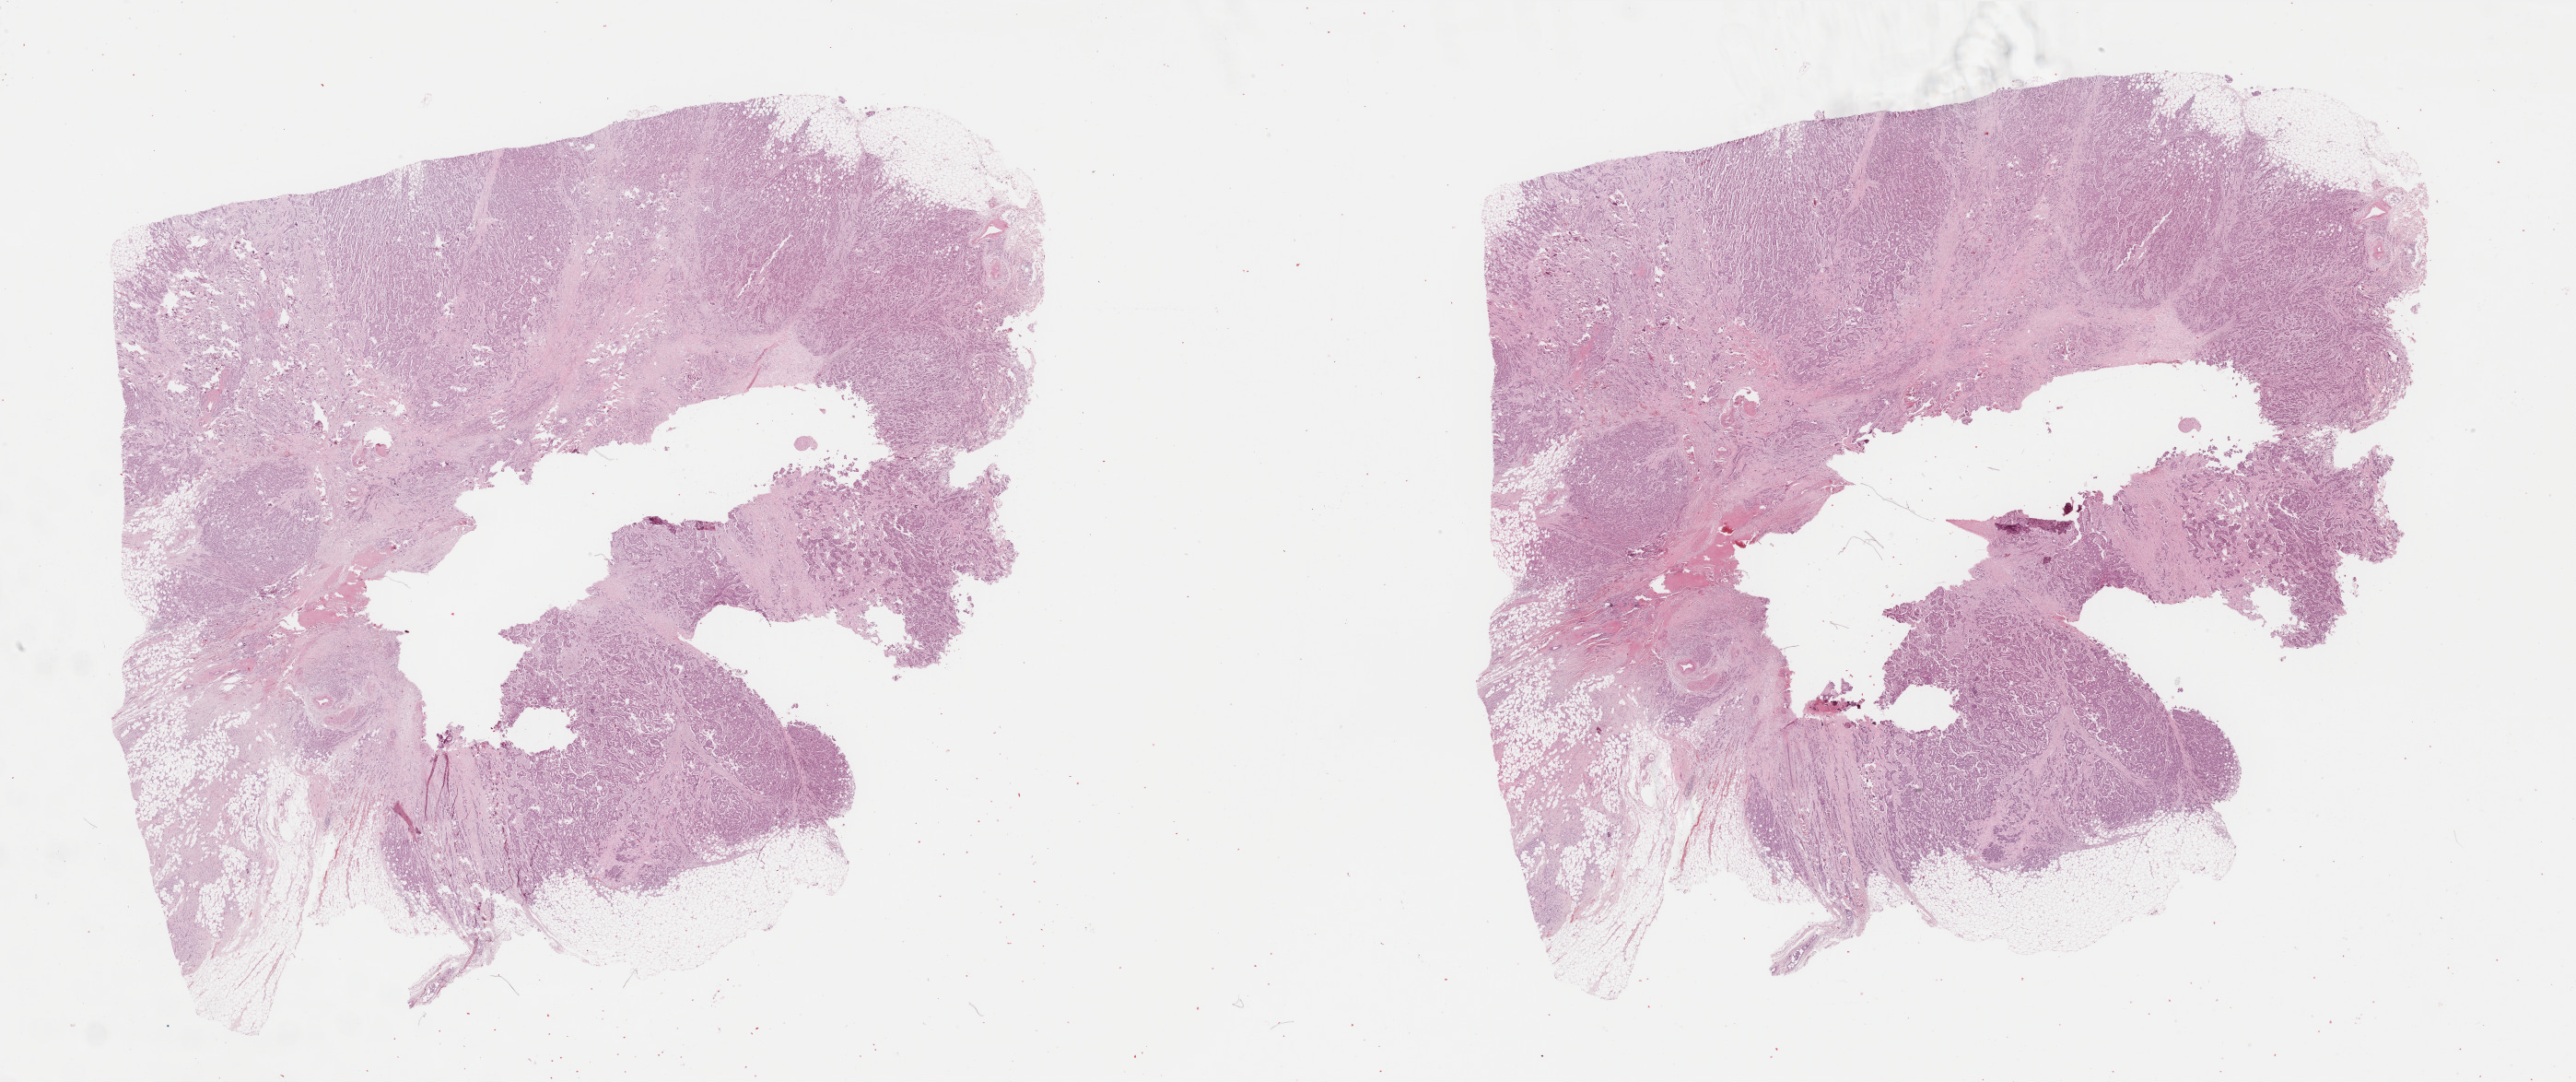
Digitized Hematoxylin and eosin (H&E) stained tissue section (whole slide), shown as a low-resolution overview of the whole scanned area (about 44.4 x 18.6 mm); formalin-fixed paraffin-embedded (FFPE) diagnostic section; breast, primary tumour sample. Patient: female, age at initial diagnosis 62 years.
• AJCC pathologic stage: IIA (7th edition)
• pathologic diagnosis: Infiltrating duct carcinoma, NOS
• lymph nodes positive (case pathology): 3 of 10 examined
• laterality: left